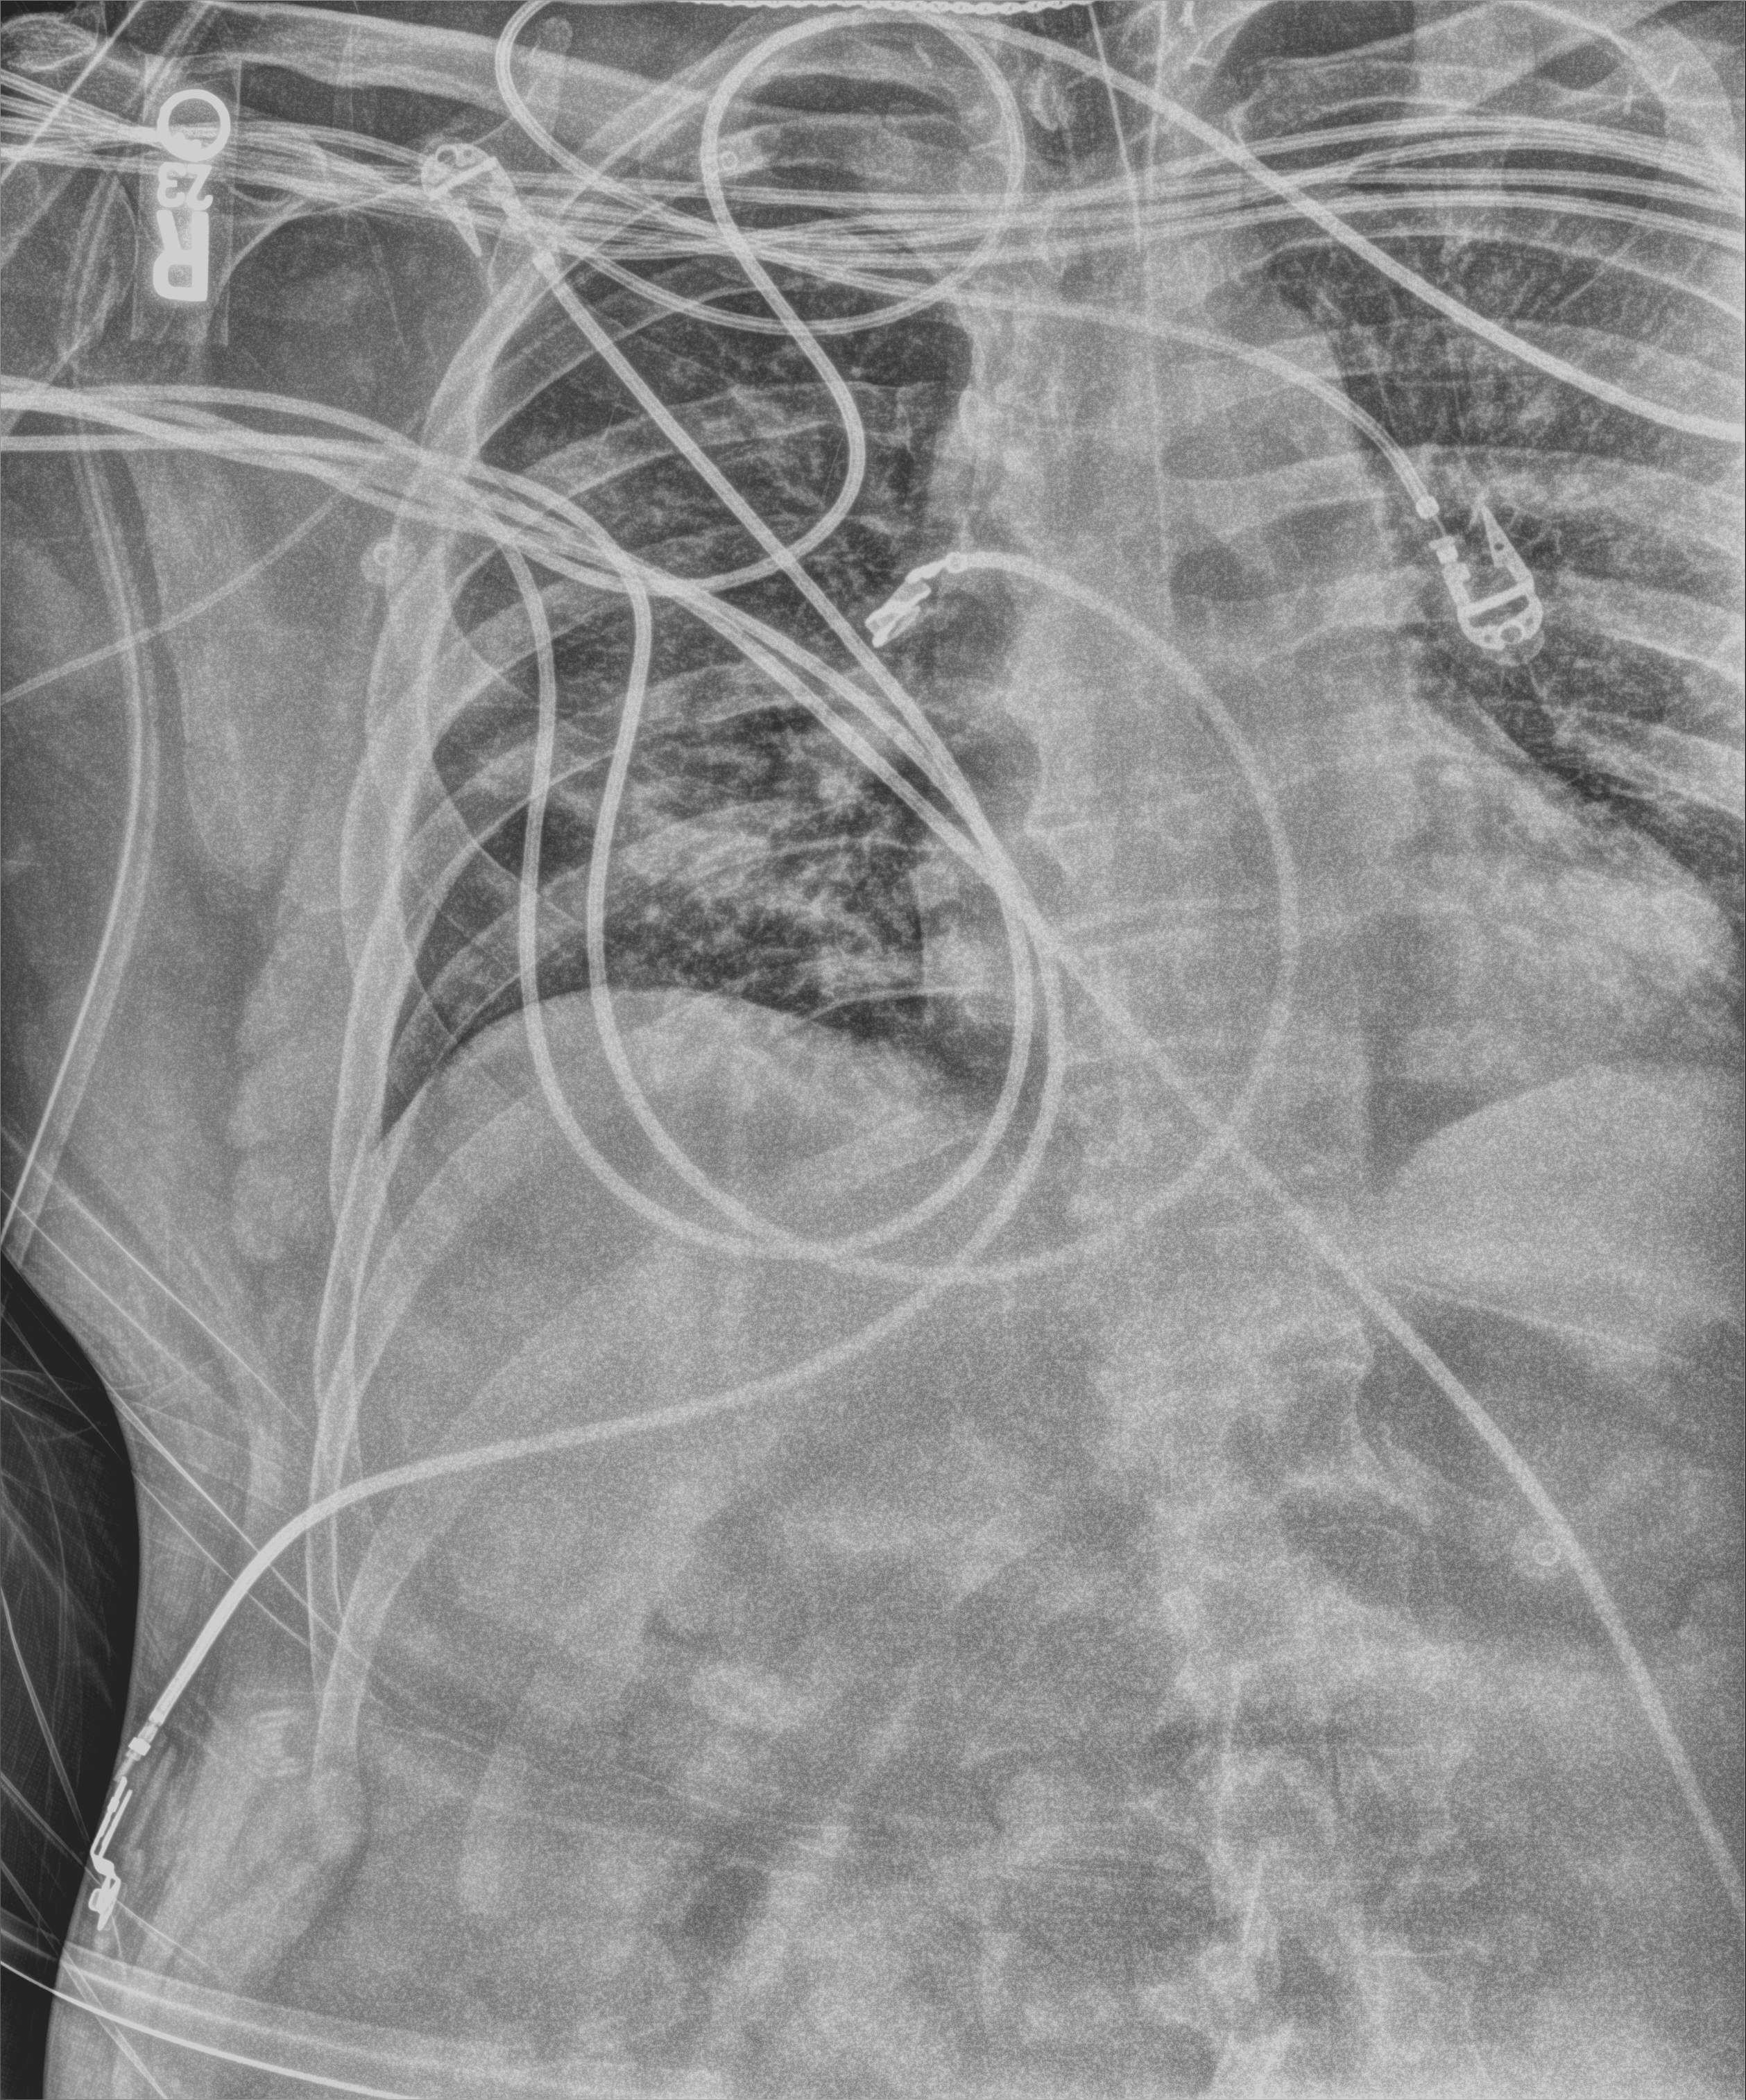
Chest X-ray (portable), anteroposterior (AP) projection. Patient hospitalised with COVID-19, aged 18–59 years.
Admission-level facts for this patient (not findings on this image; timing relative to this image not recorded): mechanically ventilated during this hospital stay: yes; smoking status (admission record): never; admitted to intensive care during this hospital stay: yes.